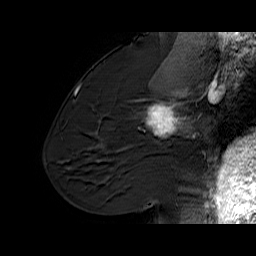
Breast MRI (dynamic contrast-enhanced), one sagittal slice; position 34 of 60 along the scan axis; dynamic contrast-enhanced series, time point 2 of 6 at this slice position (early post-contrast); 1.5 T; TE 6.1 ms, TR 32.9 ms; 4 mm slice thickness; 256 × 256 image matrix, field of view 220 × 220 mm. Female patient. From the clinical record (not read from this slice): setting: breast cancer imaged before/during neoadjuvant chemotherapy; receptor status: HER2-positive.
Structures marked on this image (semi-automatically segmented with operator editing):
- analysis volume of interest (the breast-tissue region the enhancement analysis was run in; not a lesion): box from (x=127, y=95) to (x=194, y=165) px
- tumour enhancement mask (voxels above the 100 % enhancement threshold inside the analysis volume of interest): (x=145, y=95)–(x=191, y=136)